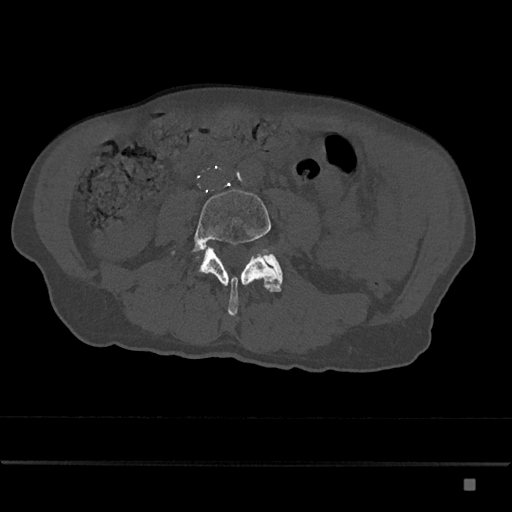
CT including the spine, one axial slice; slice 330 of 797 in the series (ordered by position); reconstruction kernel Br40s/3; bone window (W 1800 / L 400 HU); 0.5 mm slice thickness; 512 × 512 image matrix, field of view 390 × 390 mm. Male patient, age 72 years. Case-level facts recorded for this patient, not image findings: primary cancer: prostate.
Annotated regions visible in this slice (semi-automatically segmented with operator editing):
- L4 vertebra: box from (x=170, y=189) to (x=281, y=316) px
- L5 vertebra: (x=265, y=254)–(x=283, y=282)